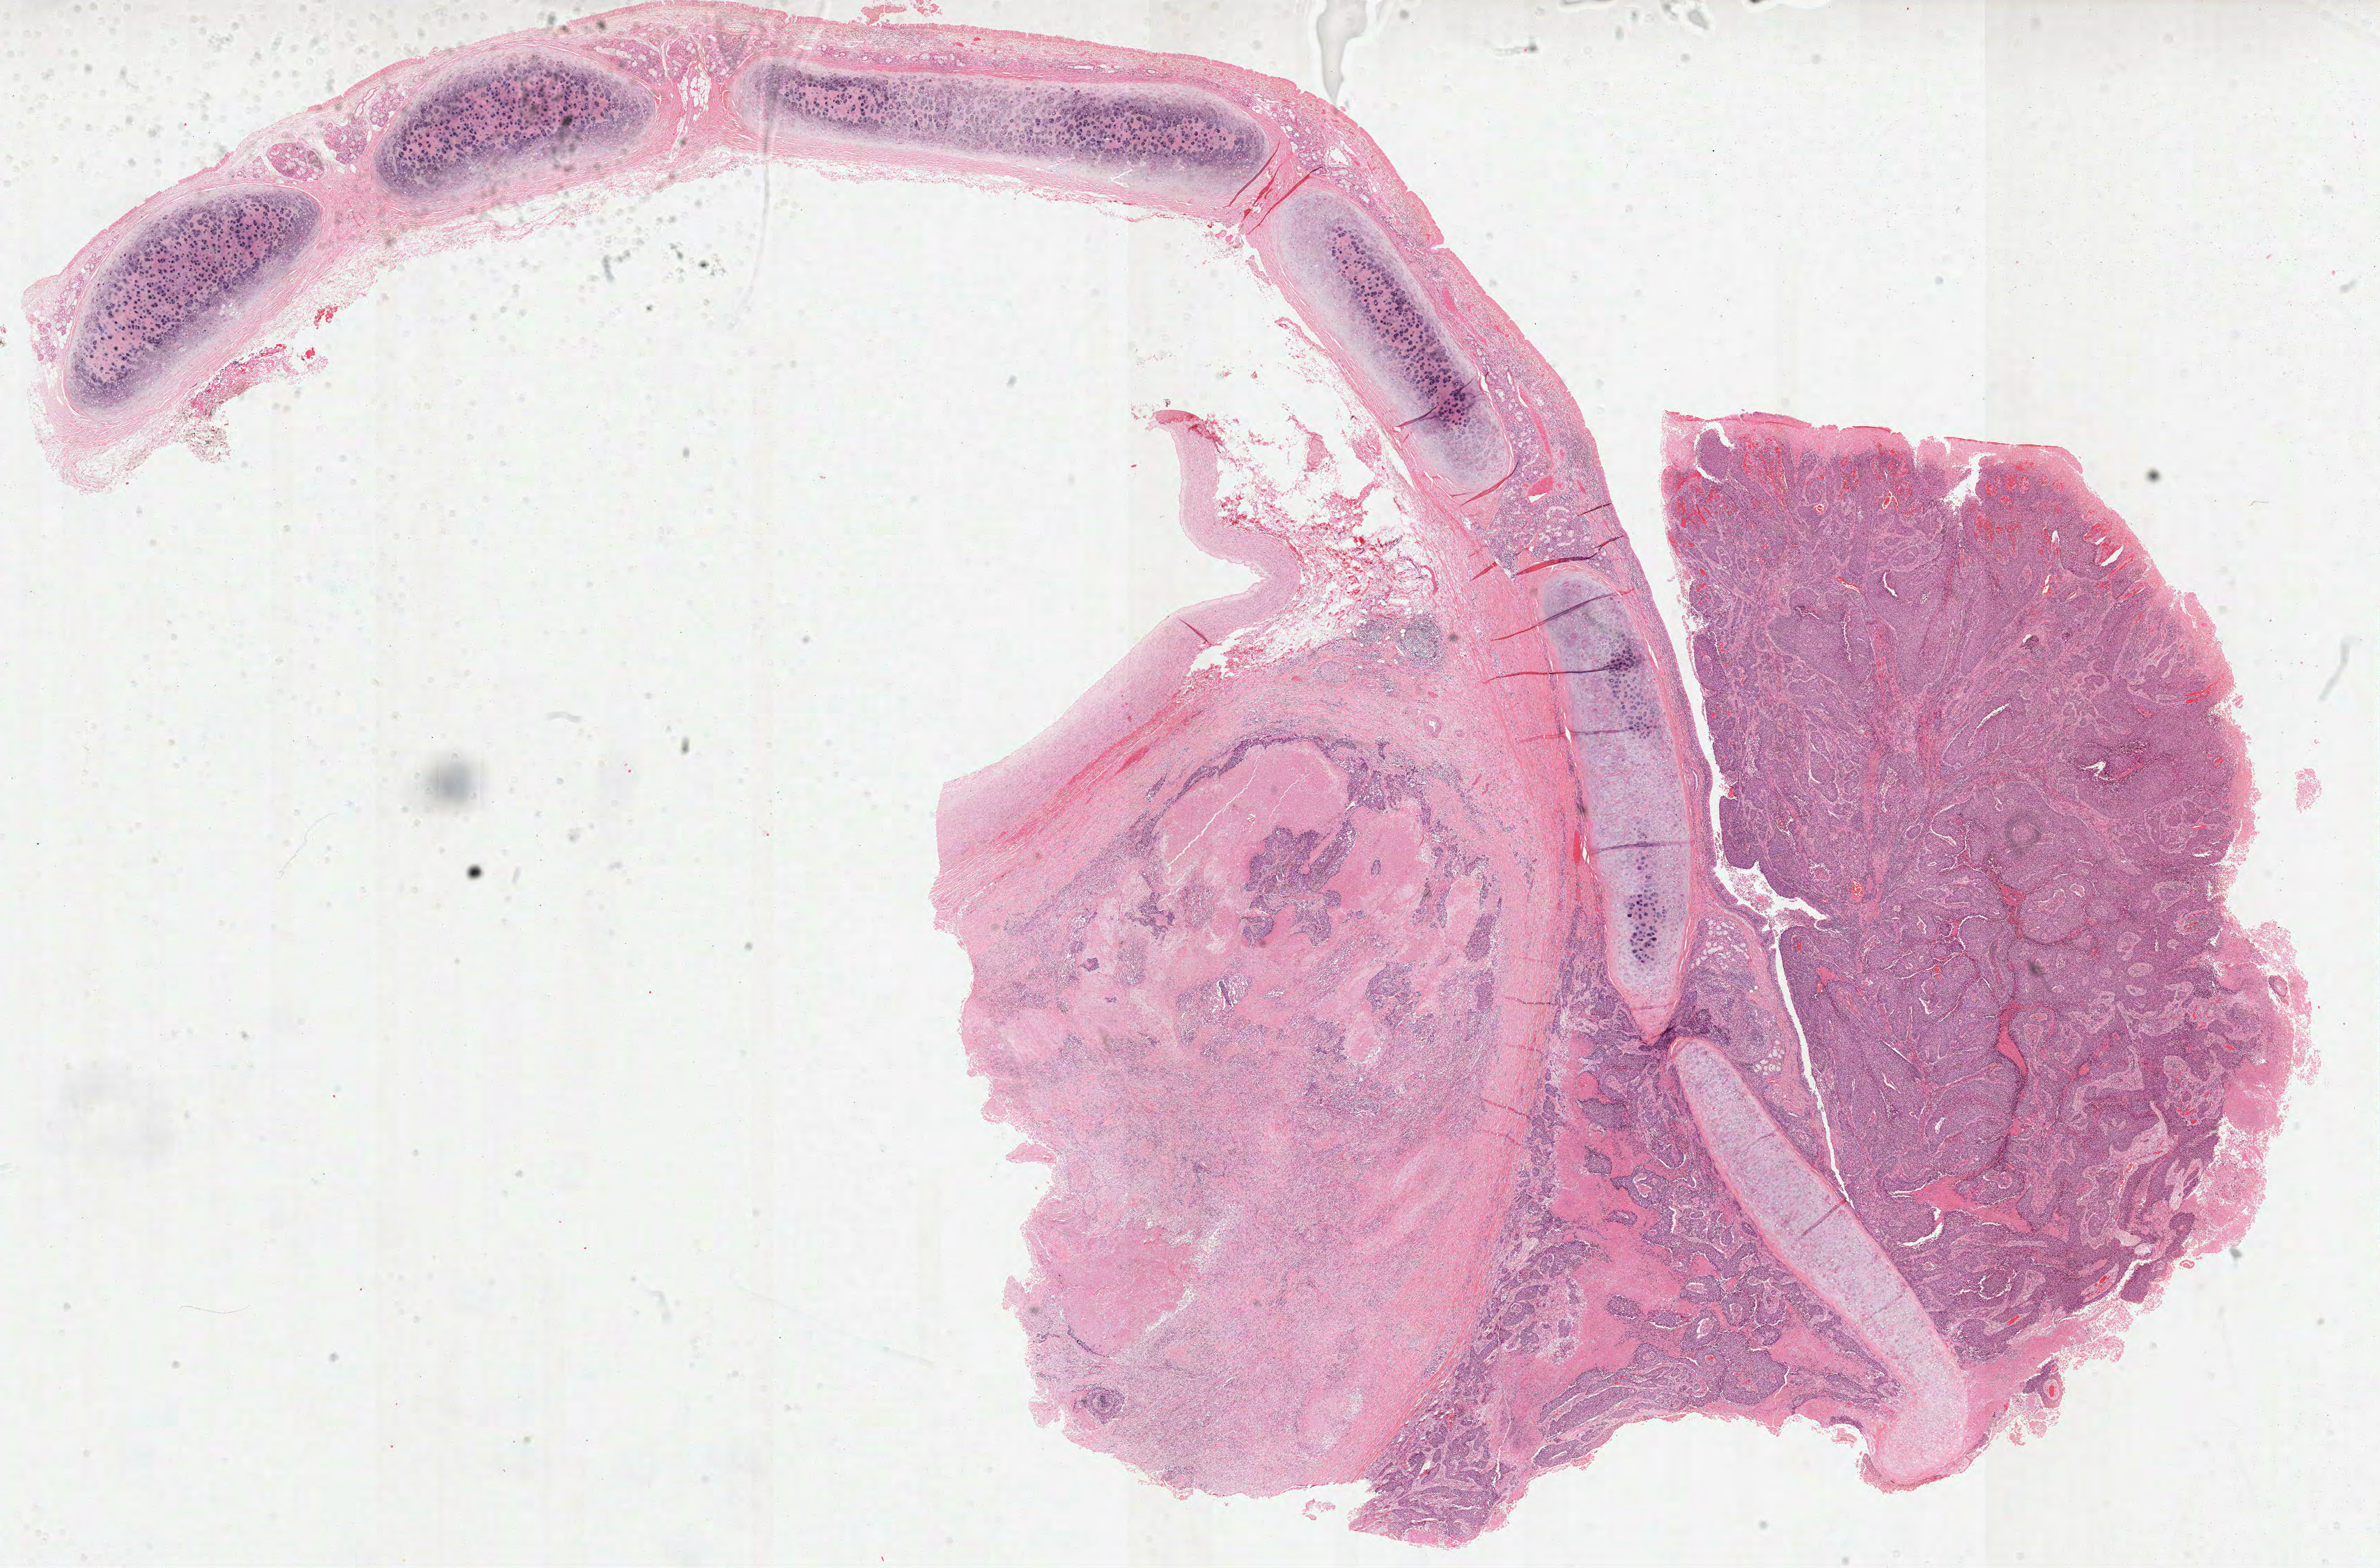
Whole-slide histology image, H&E-stained, low-resolution overview of the scanned area, about 27.6 x 18.2 mm; FFPE section; primary tumour sample from the lung. Patient: male, age at initial diagnosis 68 years.
• pathologic diagnosis: Squamous cell carcinoma, NOS
• AJCC pathologic stage: IIIA